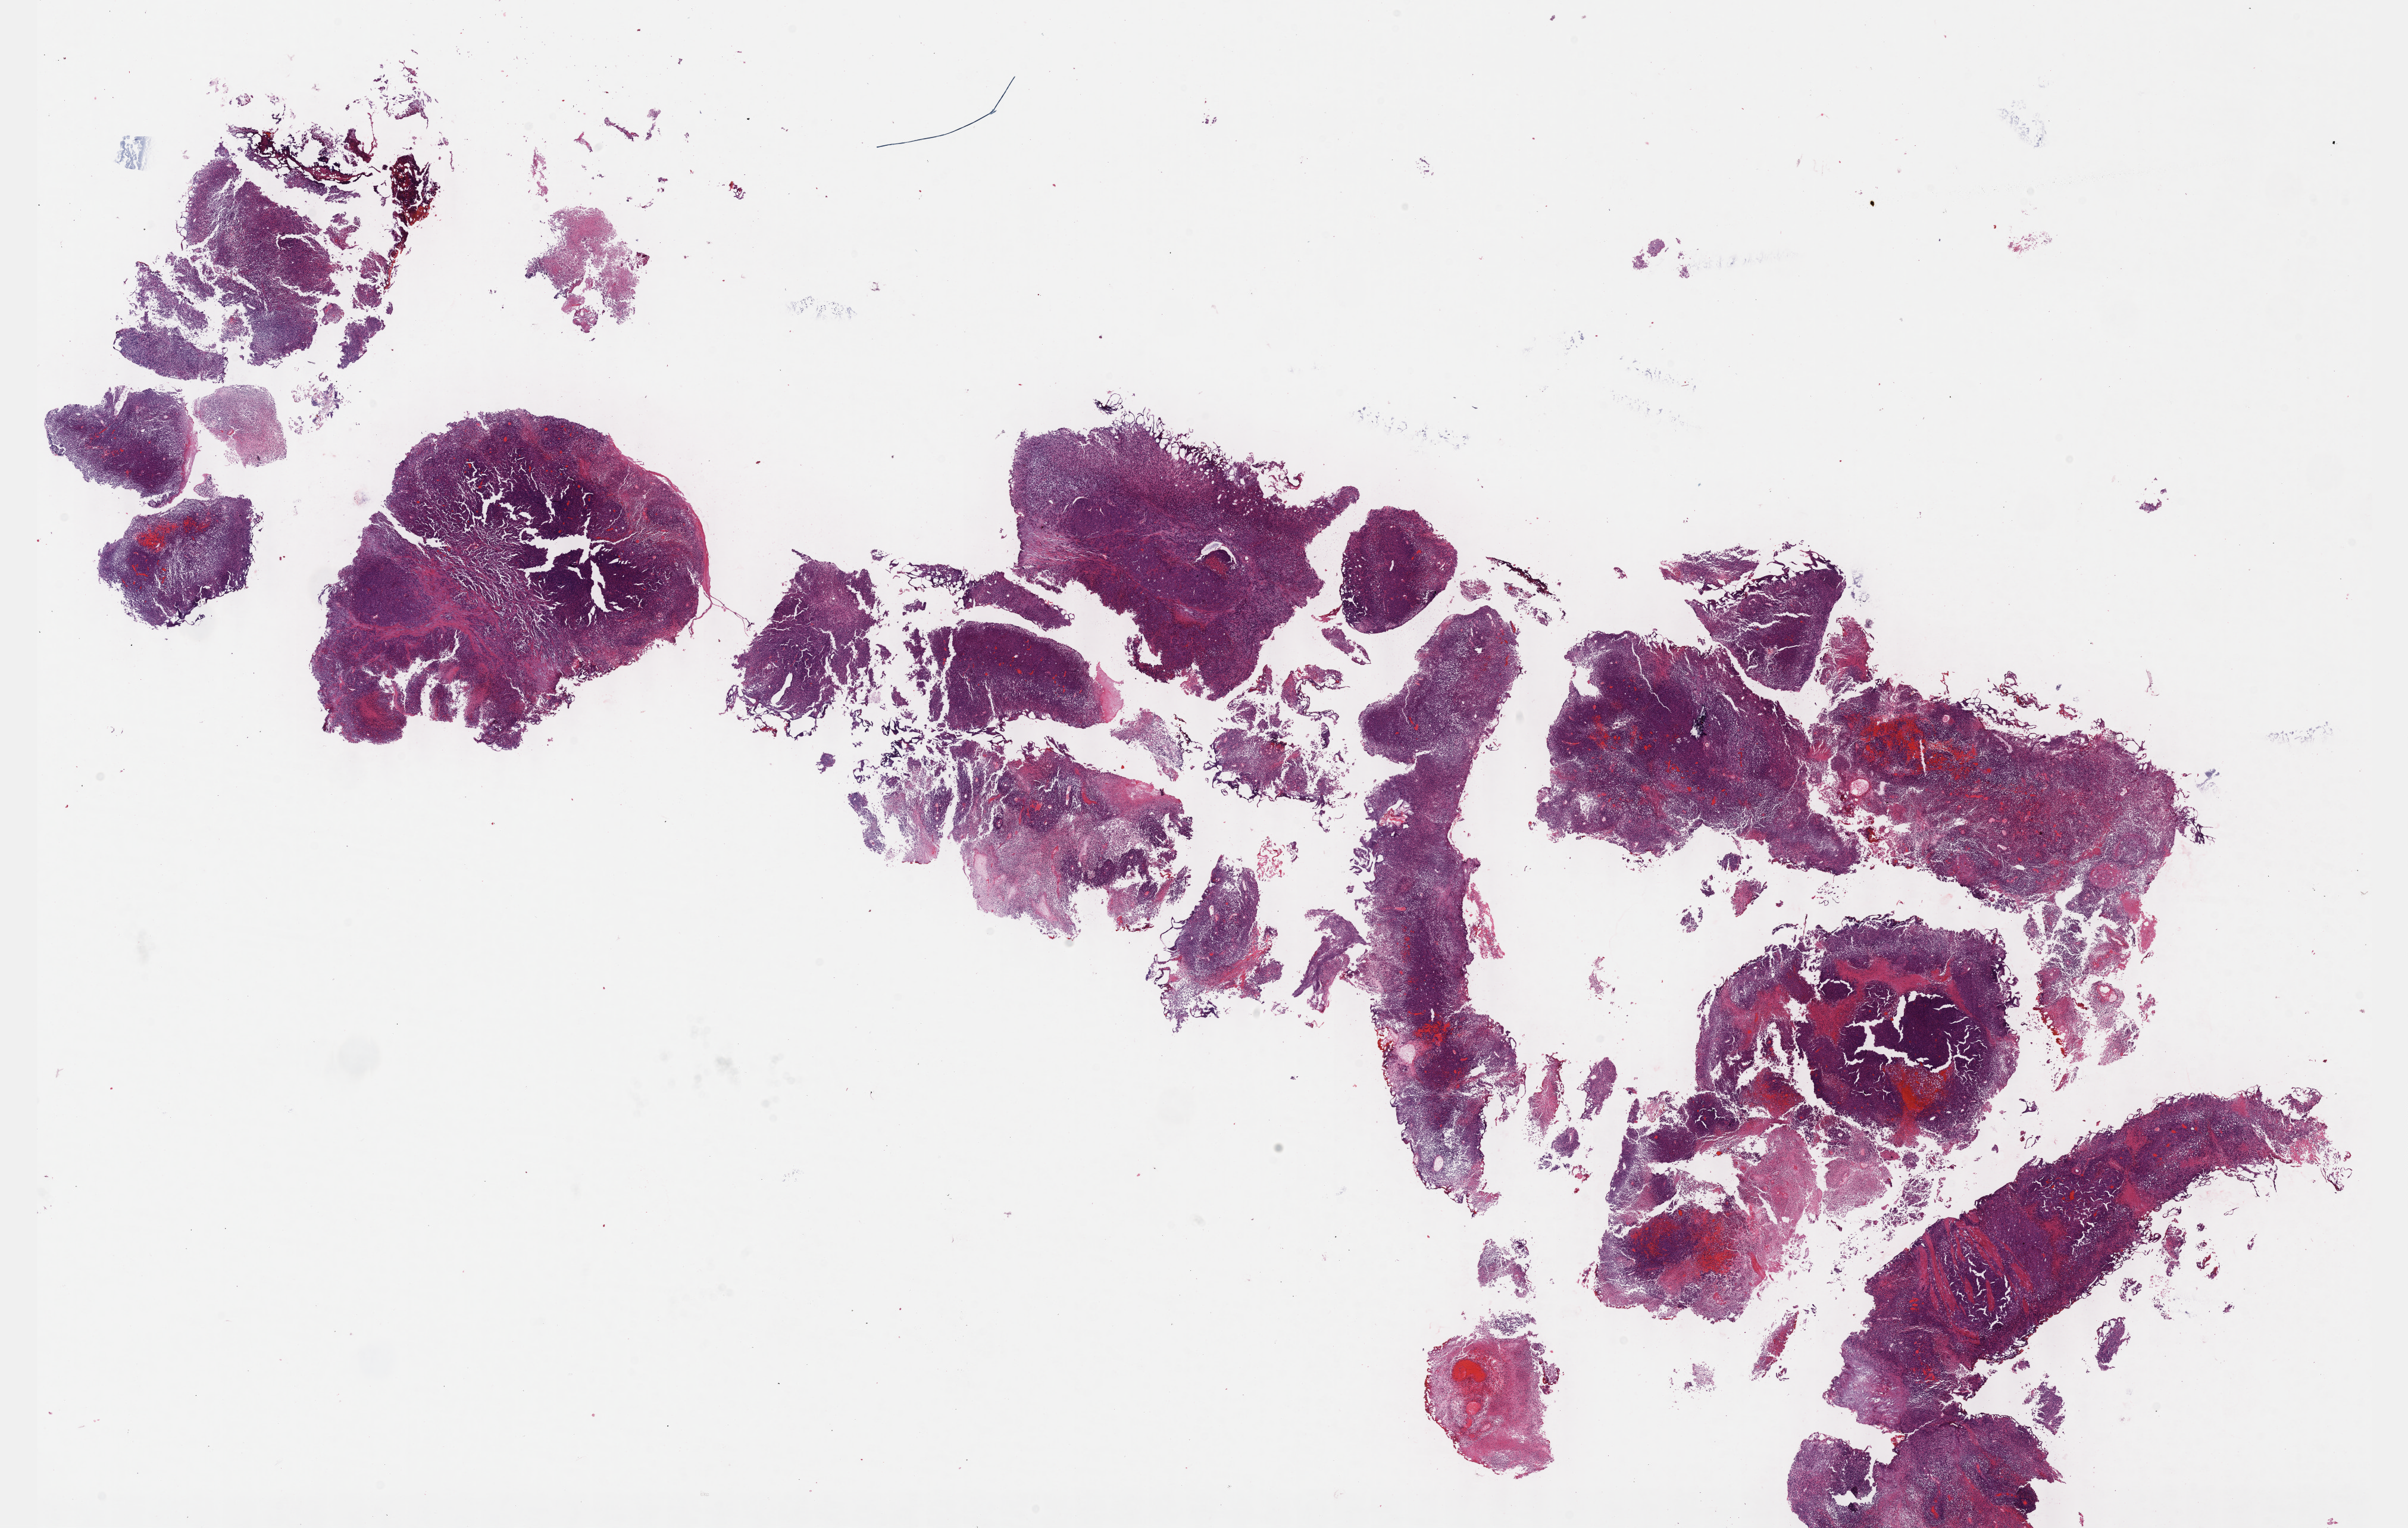
Digitized Hematoxylin and eosin (H&E) stained tissue section (whole slide), shown as a low-resolution overview of the whole scanned area (about 32.7 x 20.7 mm, from a 40x scan). Formalin-fixed paraffin-embedded (FFPE) diagnostic section. Sample: primary tumour, bladder. Male patient; age at initial diagnosis 49 years. Histologic grade: high grade.
AJCC pathologic stage: III (7th edition). Histologic diagnosis: Transitional cell carcinoma (lateral wall of bladder).